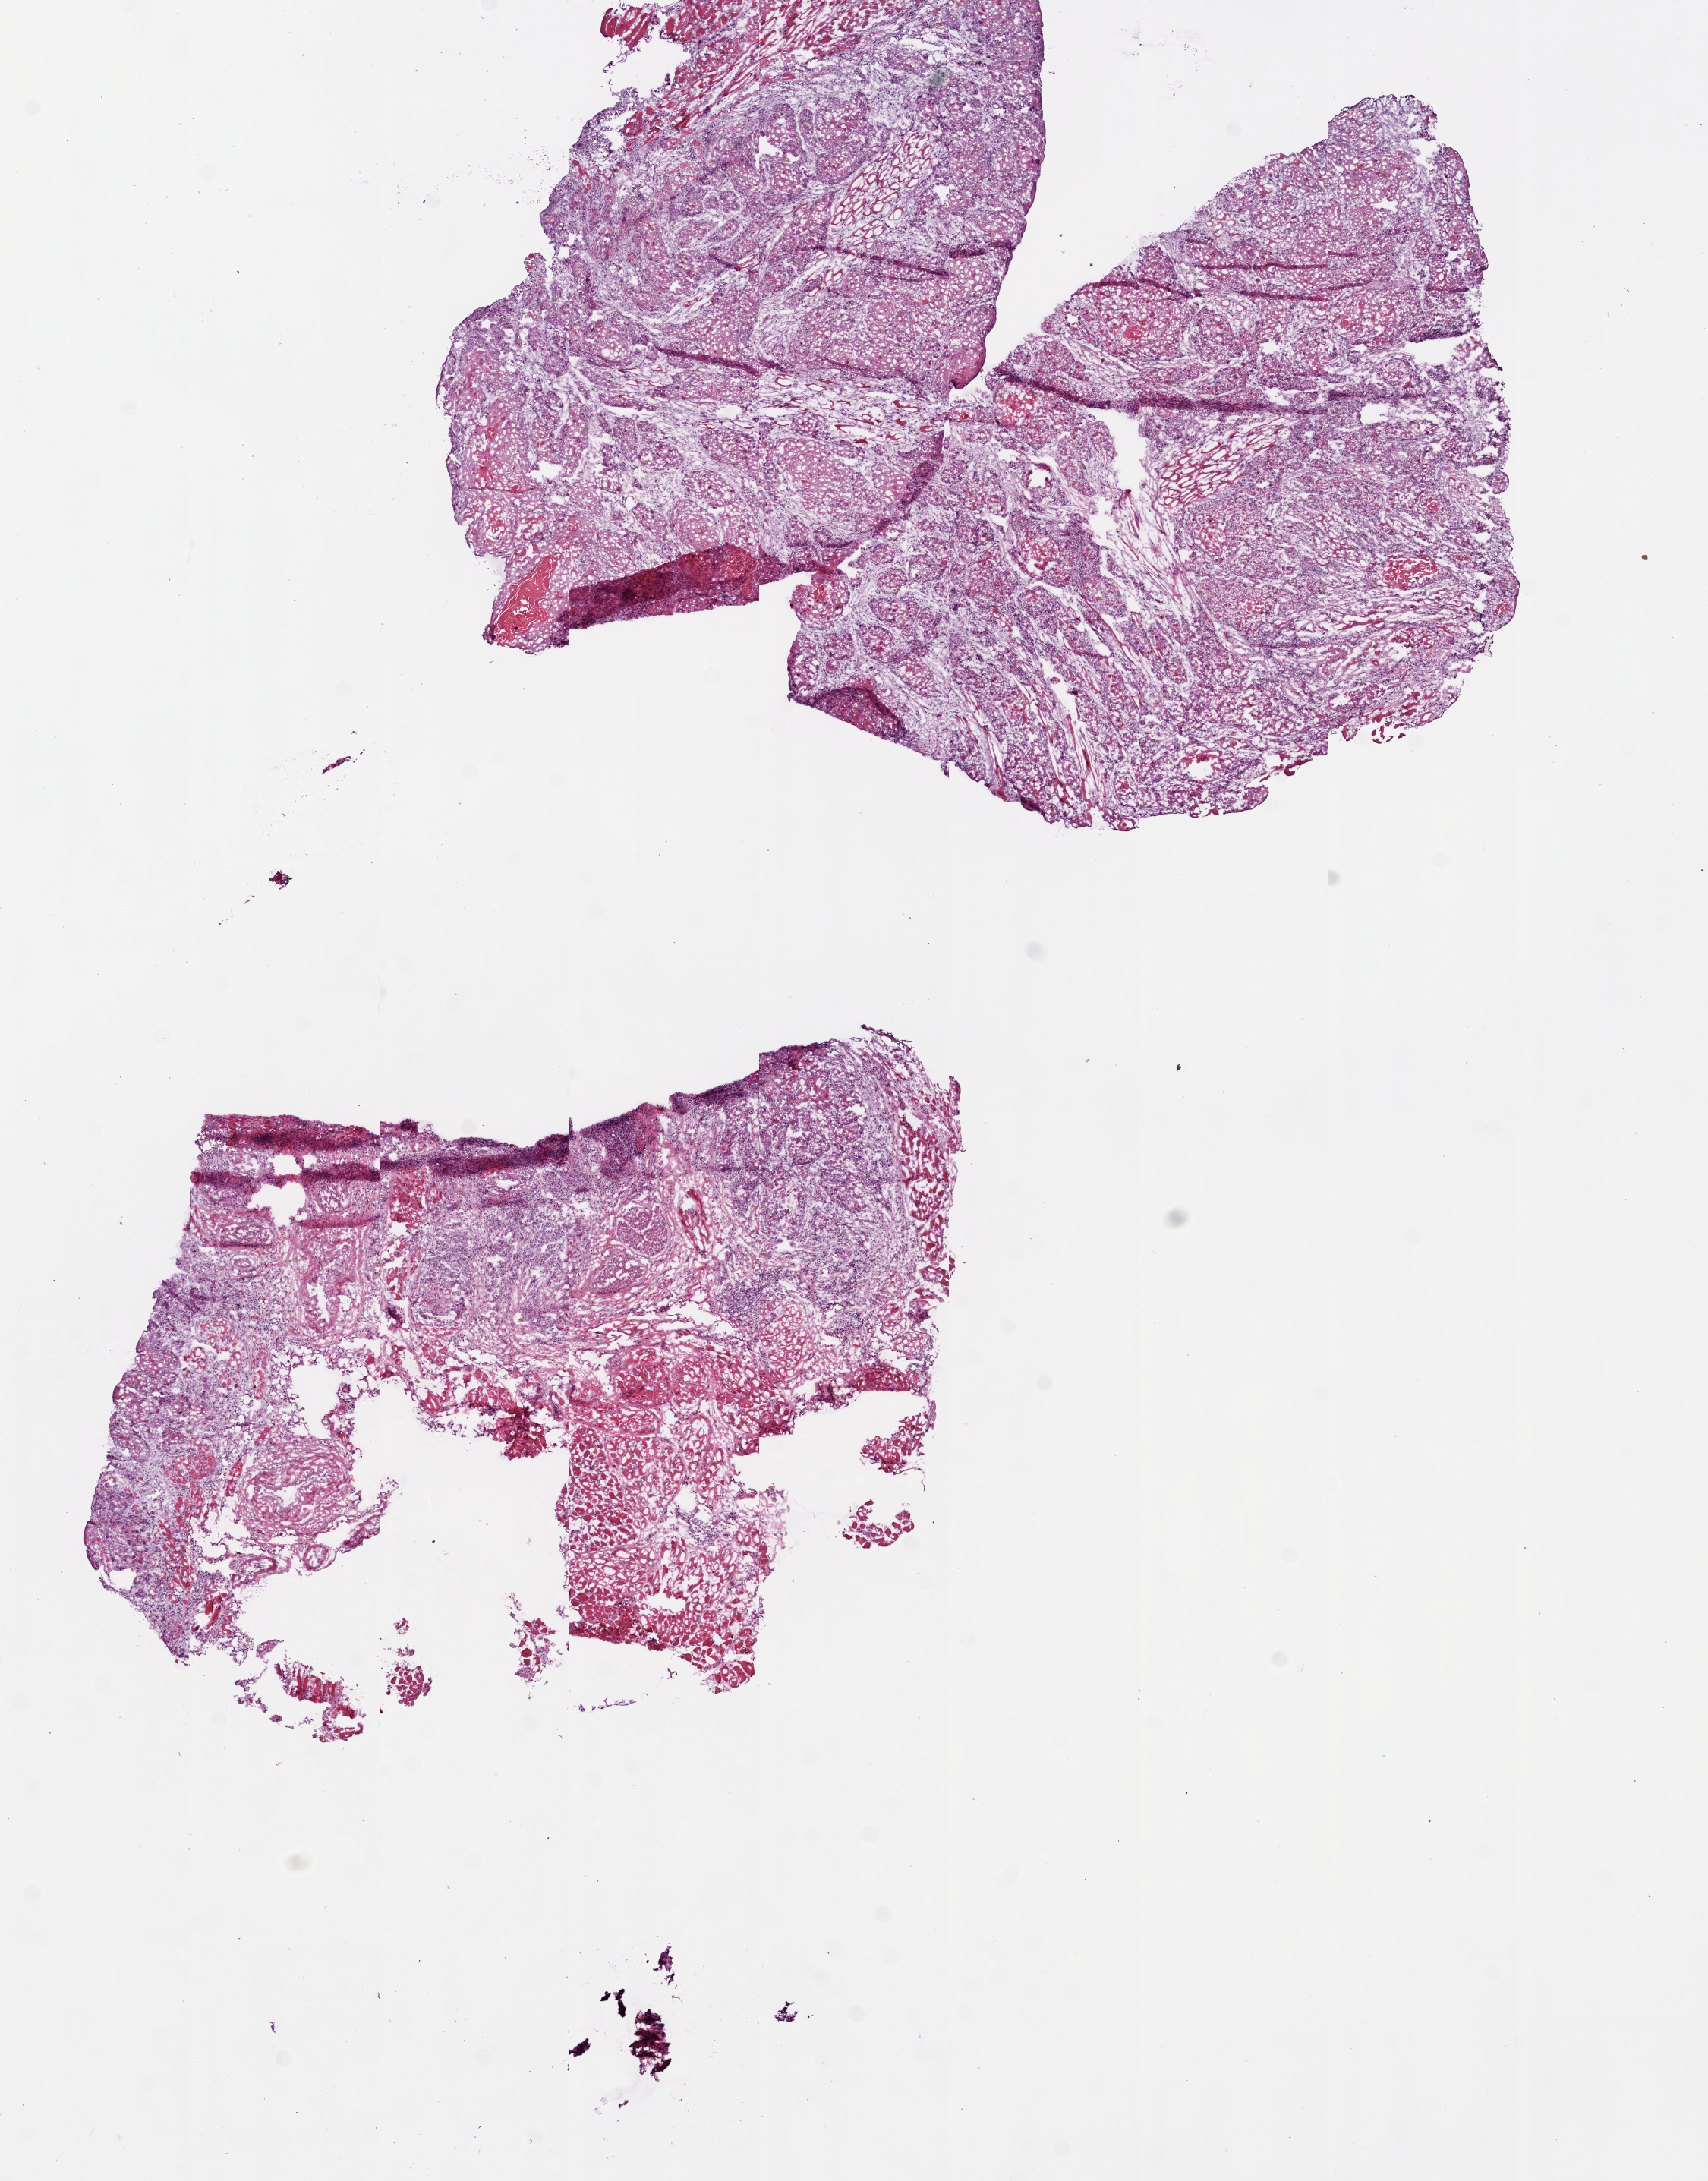
Digitized H&E-stained tissue section (whole slide) — low-resolution overview of the scanned area, about 9.0 x 11.5 mm (from a 20x scan). Frozen section. Head and neck, primary tumour sample. Female patient; age at initial diagnosis 70 years. Histologic grade: G2 (moderately differentiated). Pathologist review of this section (percent, as recorded): tumour cells 82%, tumour nuclei 75%, normal cells 0%, stromal cells 15%, necrosis 3%.
Diagnosis: Squamous cell carcinoma, NOS.